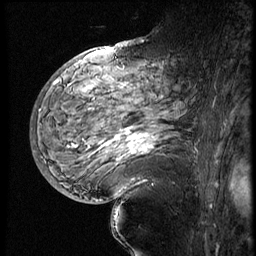
Breast MRI (dynamic contrast-enhanced), one sagittal slice. 4 images stored at this slice position (order not interpretable as contrast timing). 1.5 T. TE 4.2 ms, TR 9 ms. 2.5 mm slice thickness. 256 × 256 image matrix. Female patient, age 56 years. From the clinical record (not read from this slice): setting: breast cancer imaged before/during neoadjuvant chemotherapy; receptor status: HER2-positive.
Structures marked on this image (semi-automatically segmented with operator editing):
- analysis volume of interest (the breast-tissue region the enhancement analysis was run in; not a lesion): bounding box (x1, y1, x2, y2) in pixels: (82, 83, 199, 177)
- tumour enhancement mask (voxels above the 140 % enhancement threshold inside the analysis volume of interest): (105, 132, 154, 162)